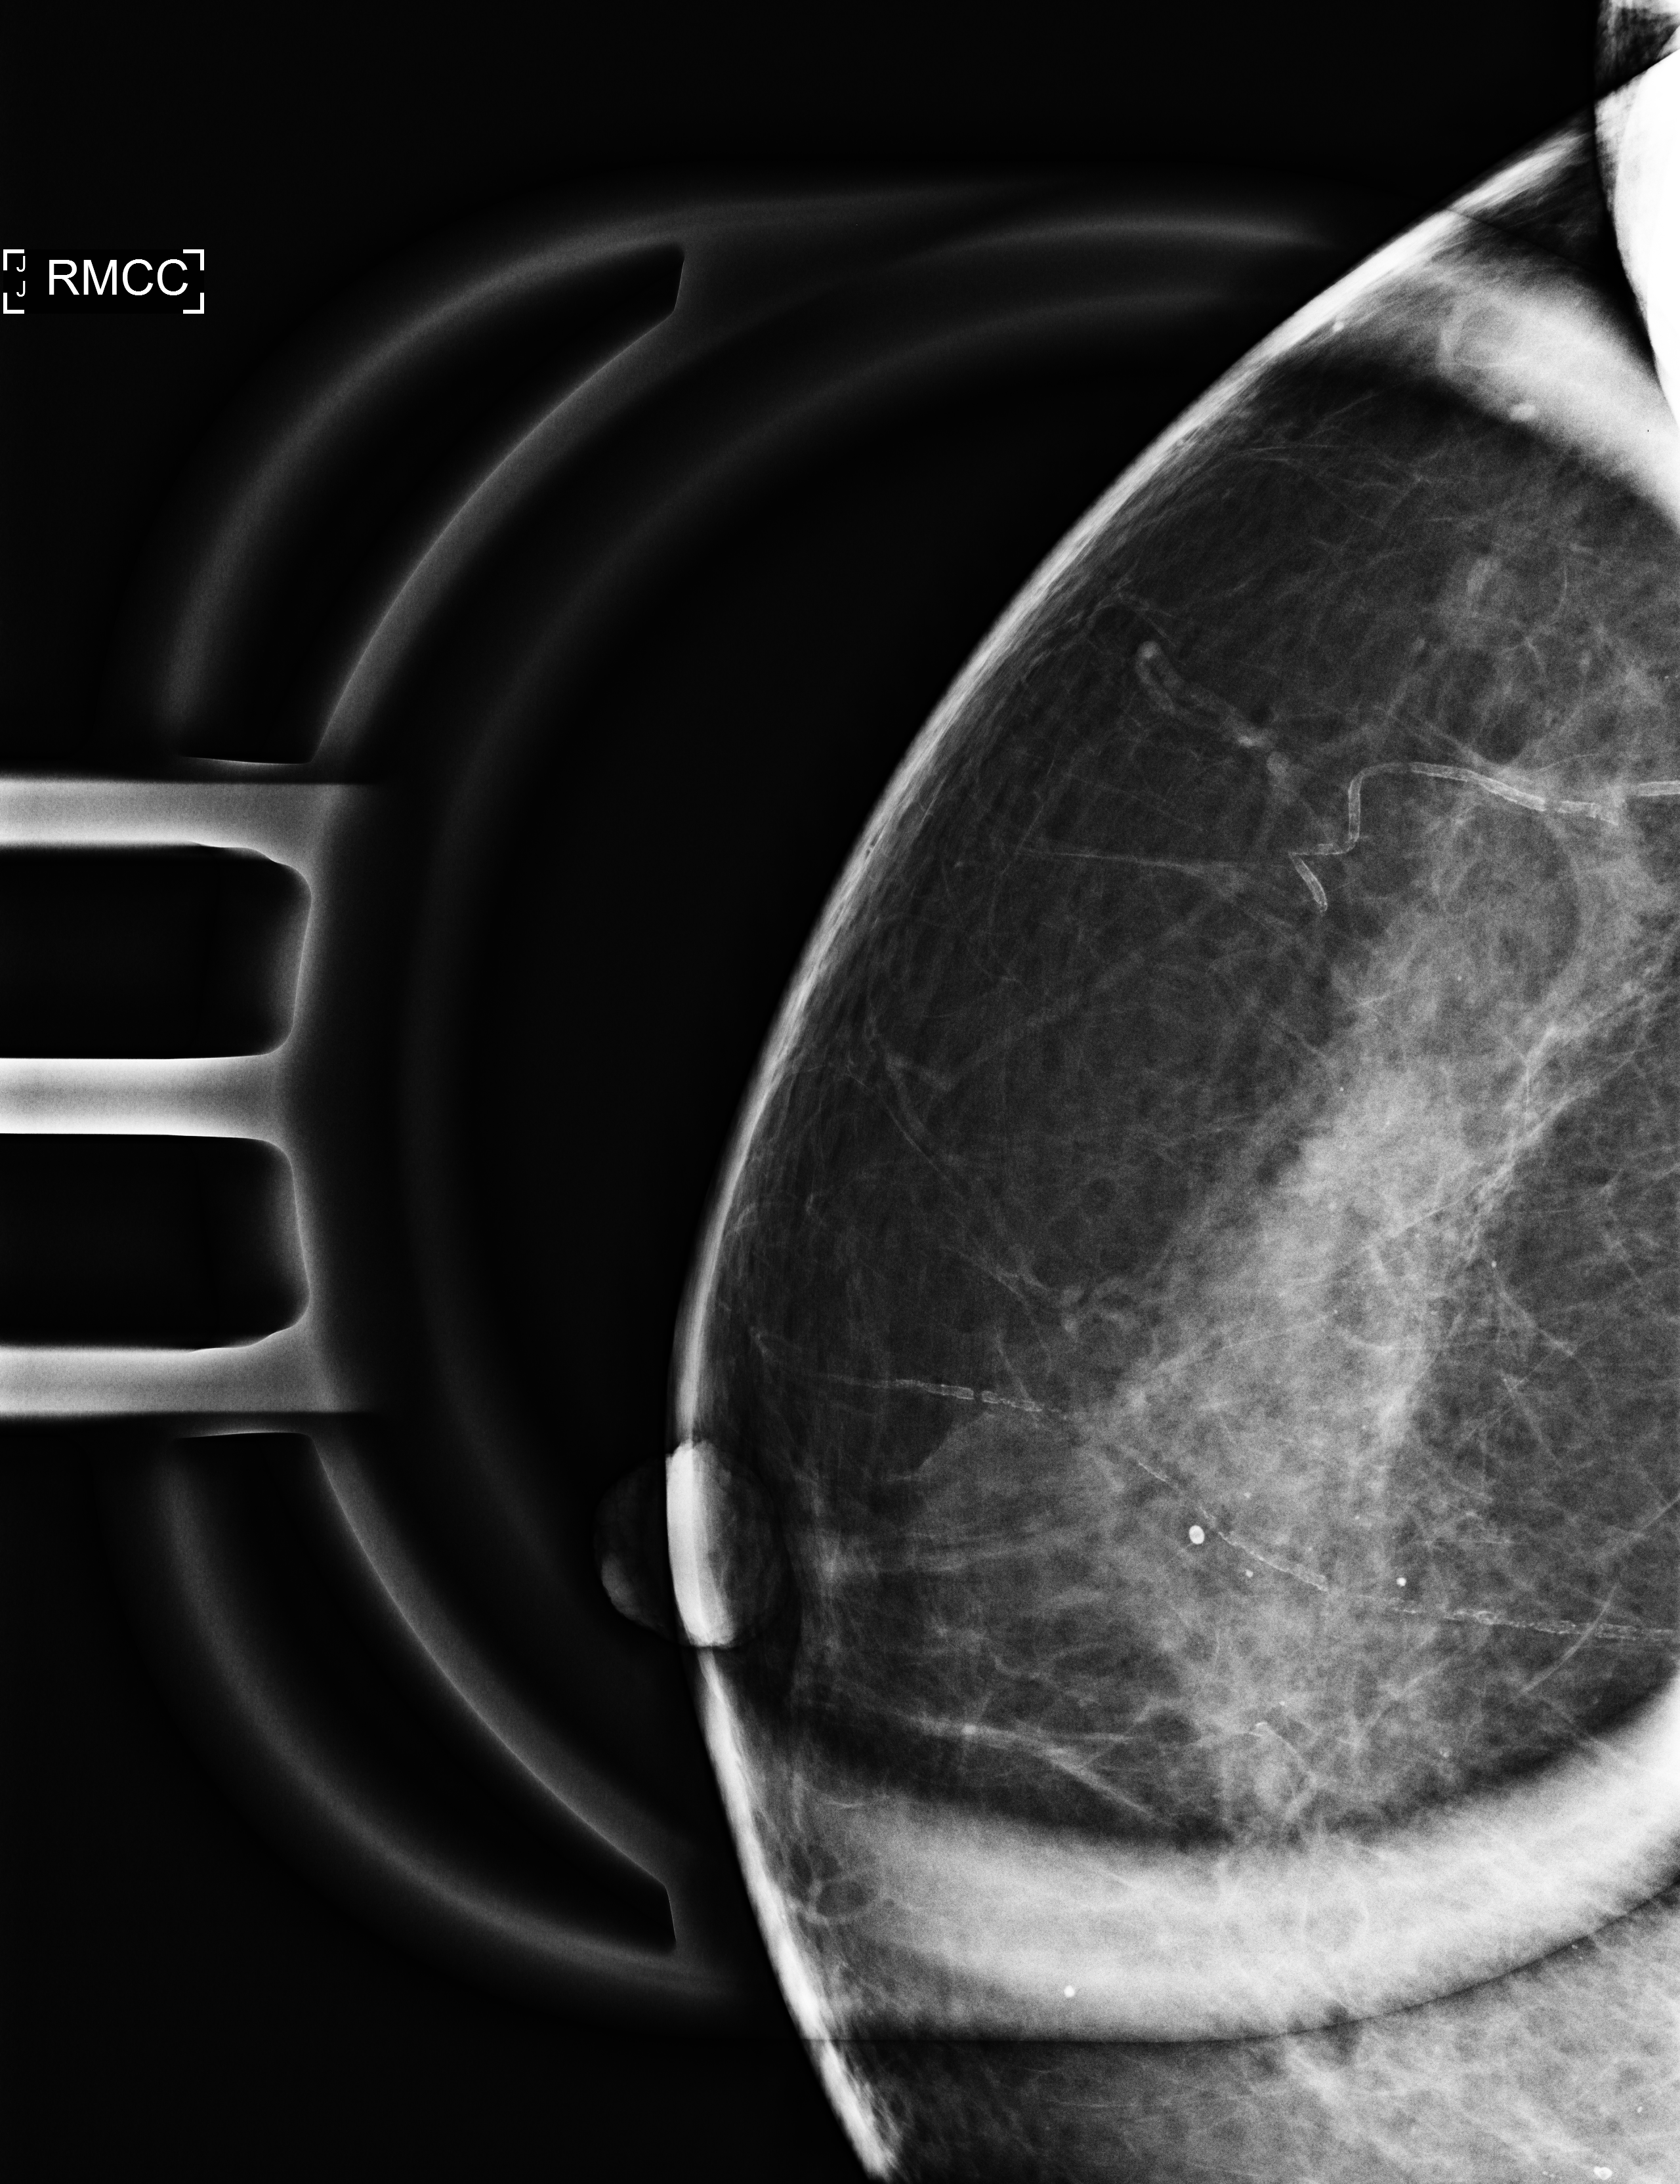
Additional (diagnostic) view; system: Selenia Dimensions. Patient: female, 68 years.
Image type: full-field digital mammogram. Breast: right. Projection: CC view, magnification.